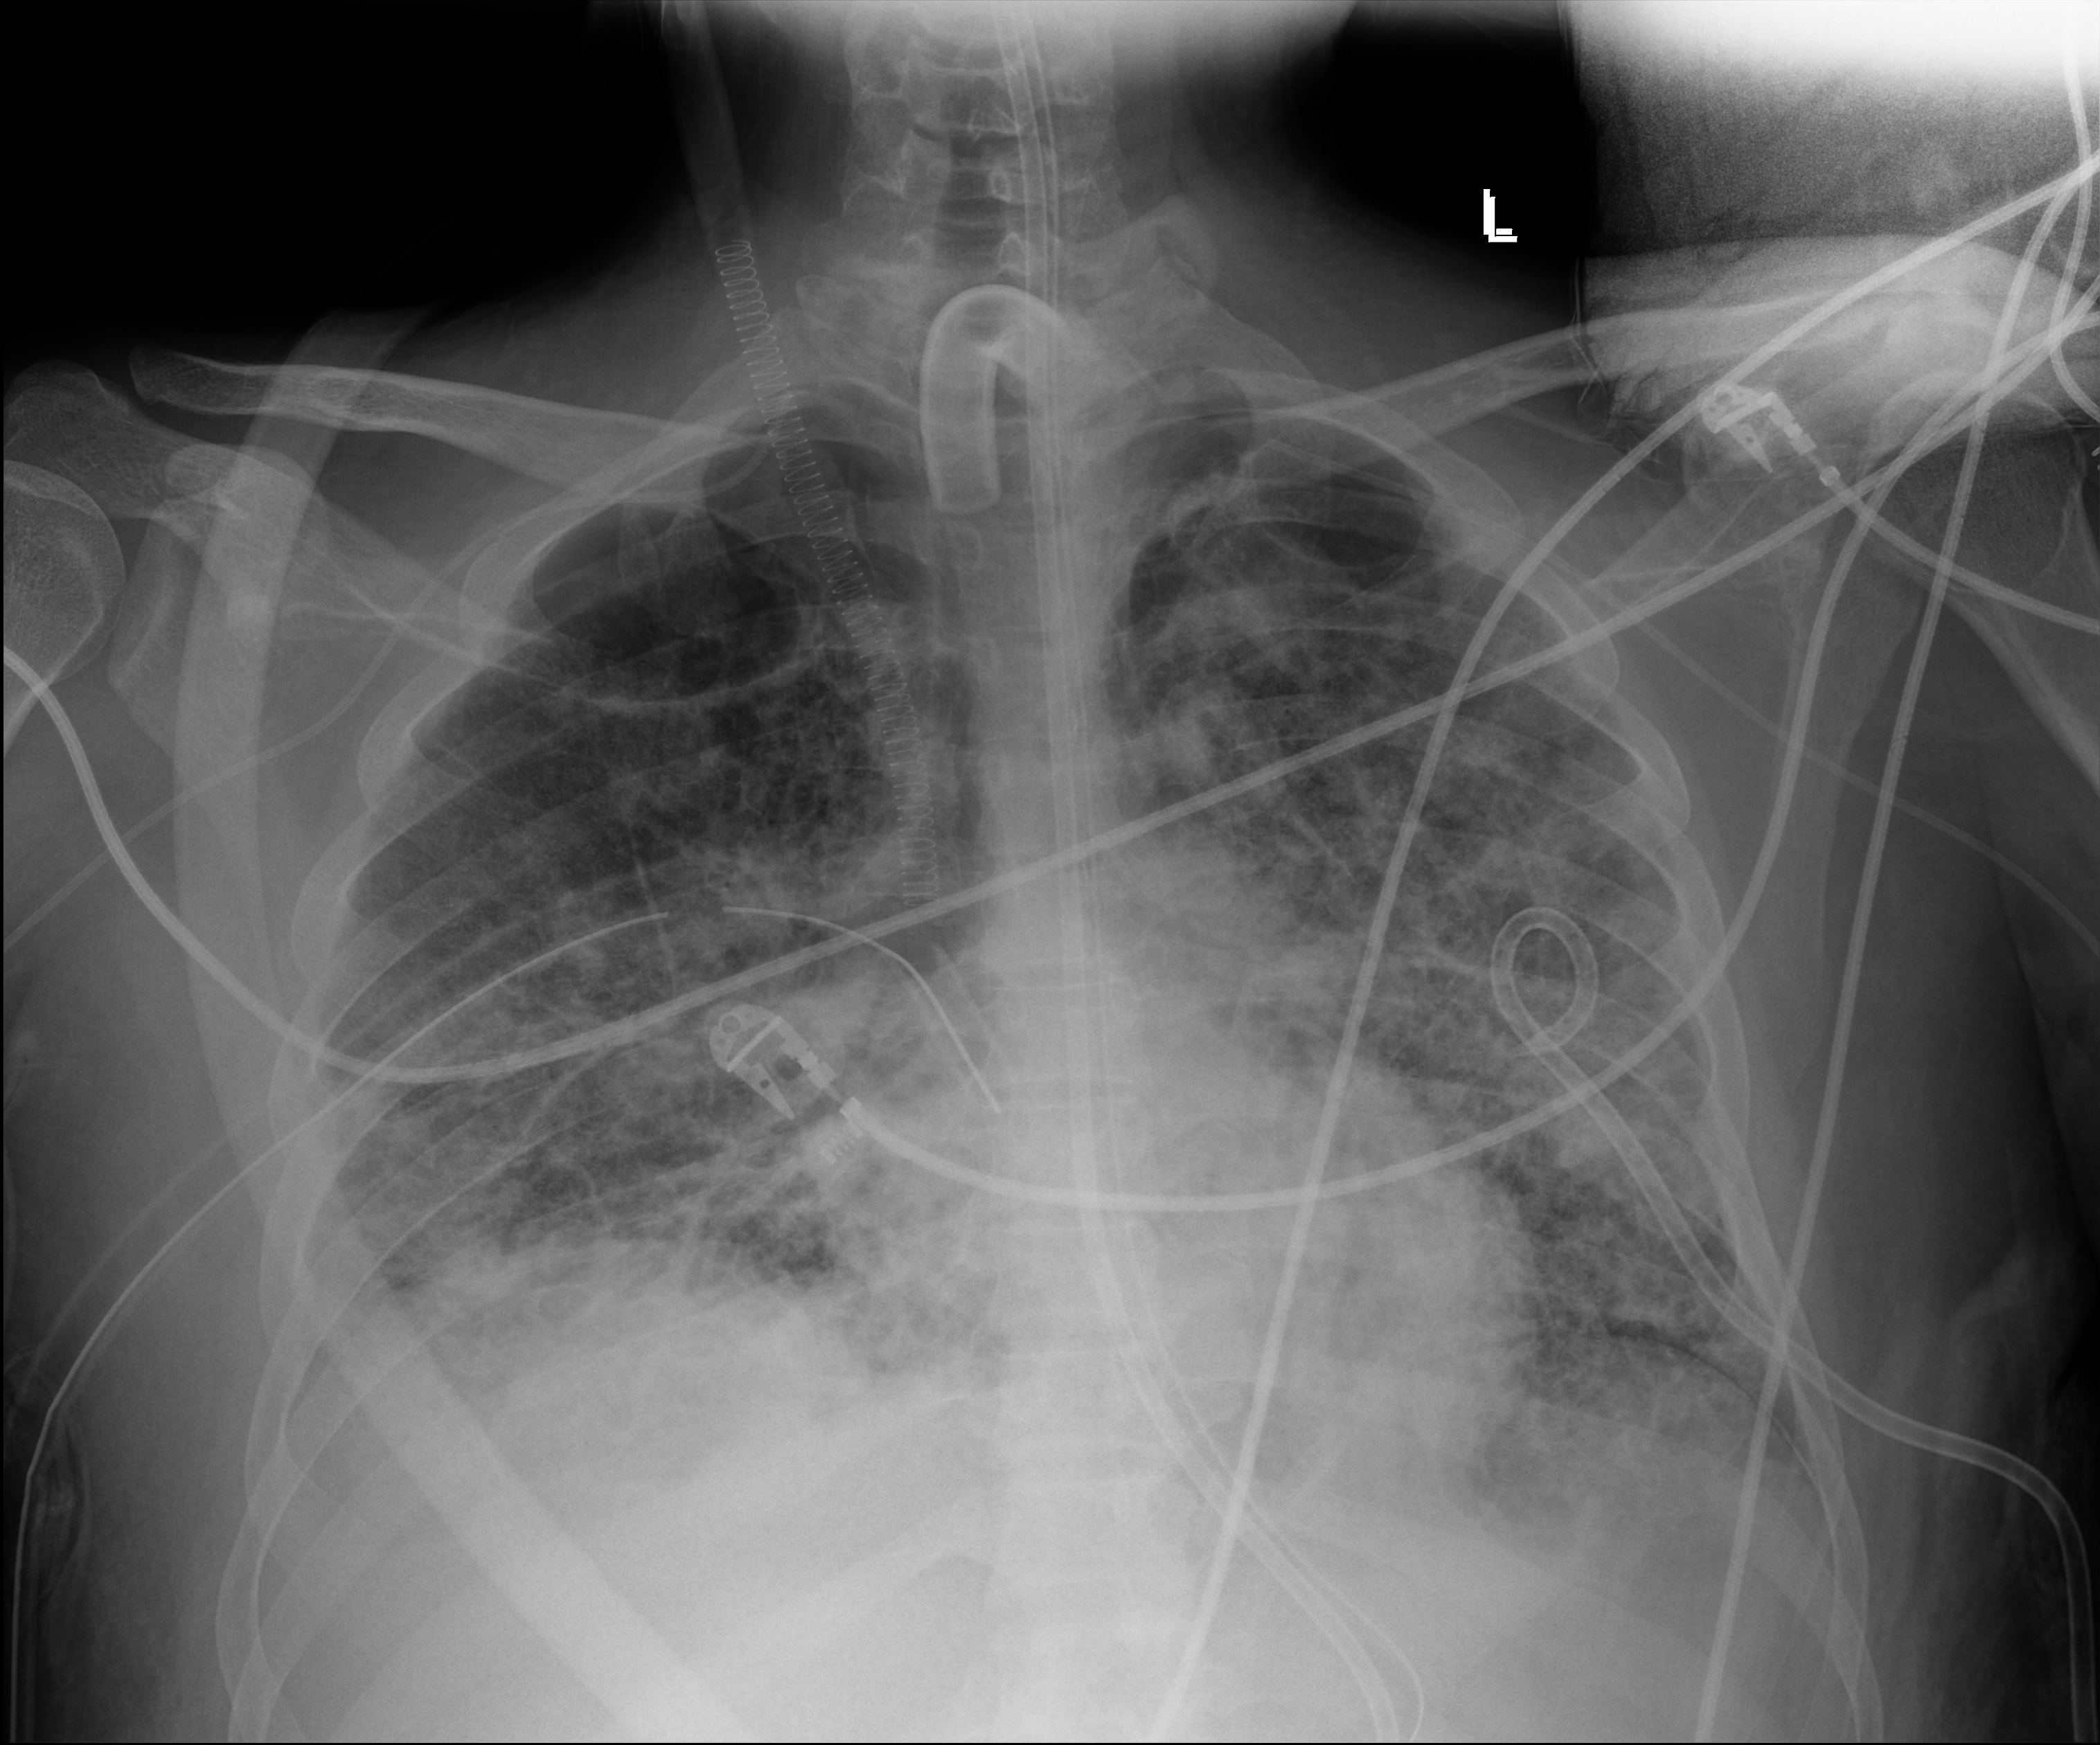
Chest radiograph (digital radiography); anteroposterior (AP) projection. Adult patient hospitalised with COVID-19, age 18–59 years.
Admission-level facts for this patient (not findings on this image; timing relative to this image not recorded): length of hospital stay: 60 days; admitted to intensive care during this hospital stay: yes; mechanically ventilated during this hospital stay: yes.